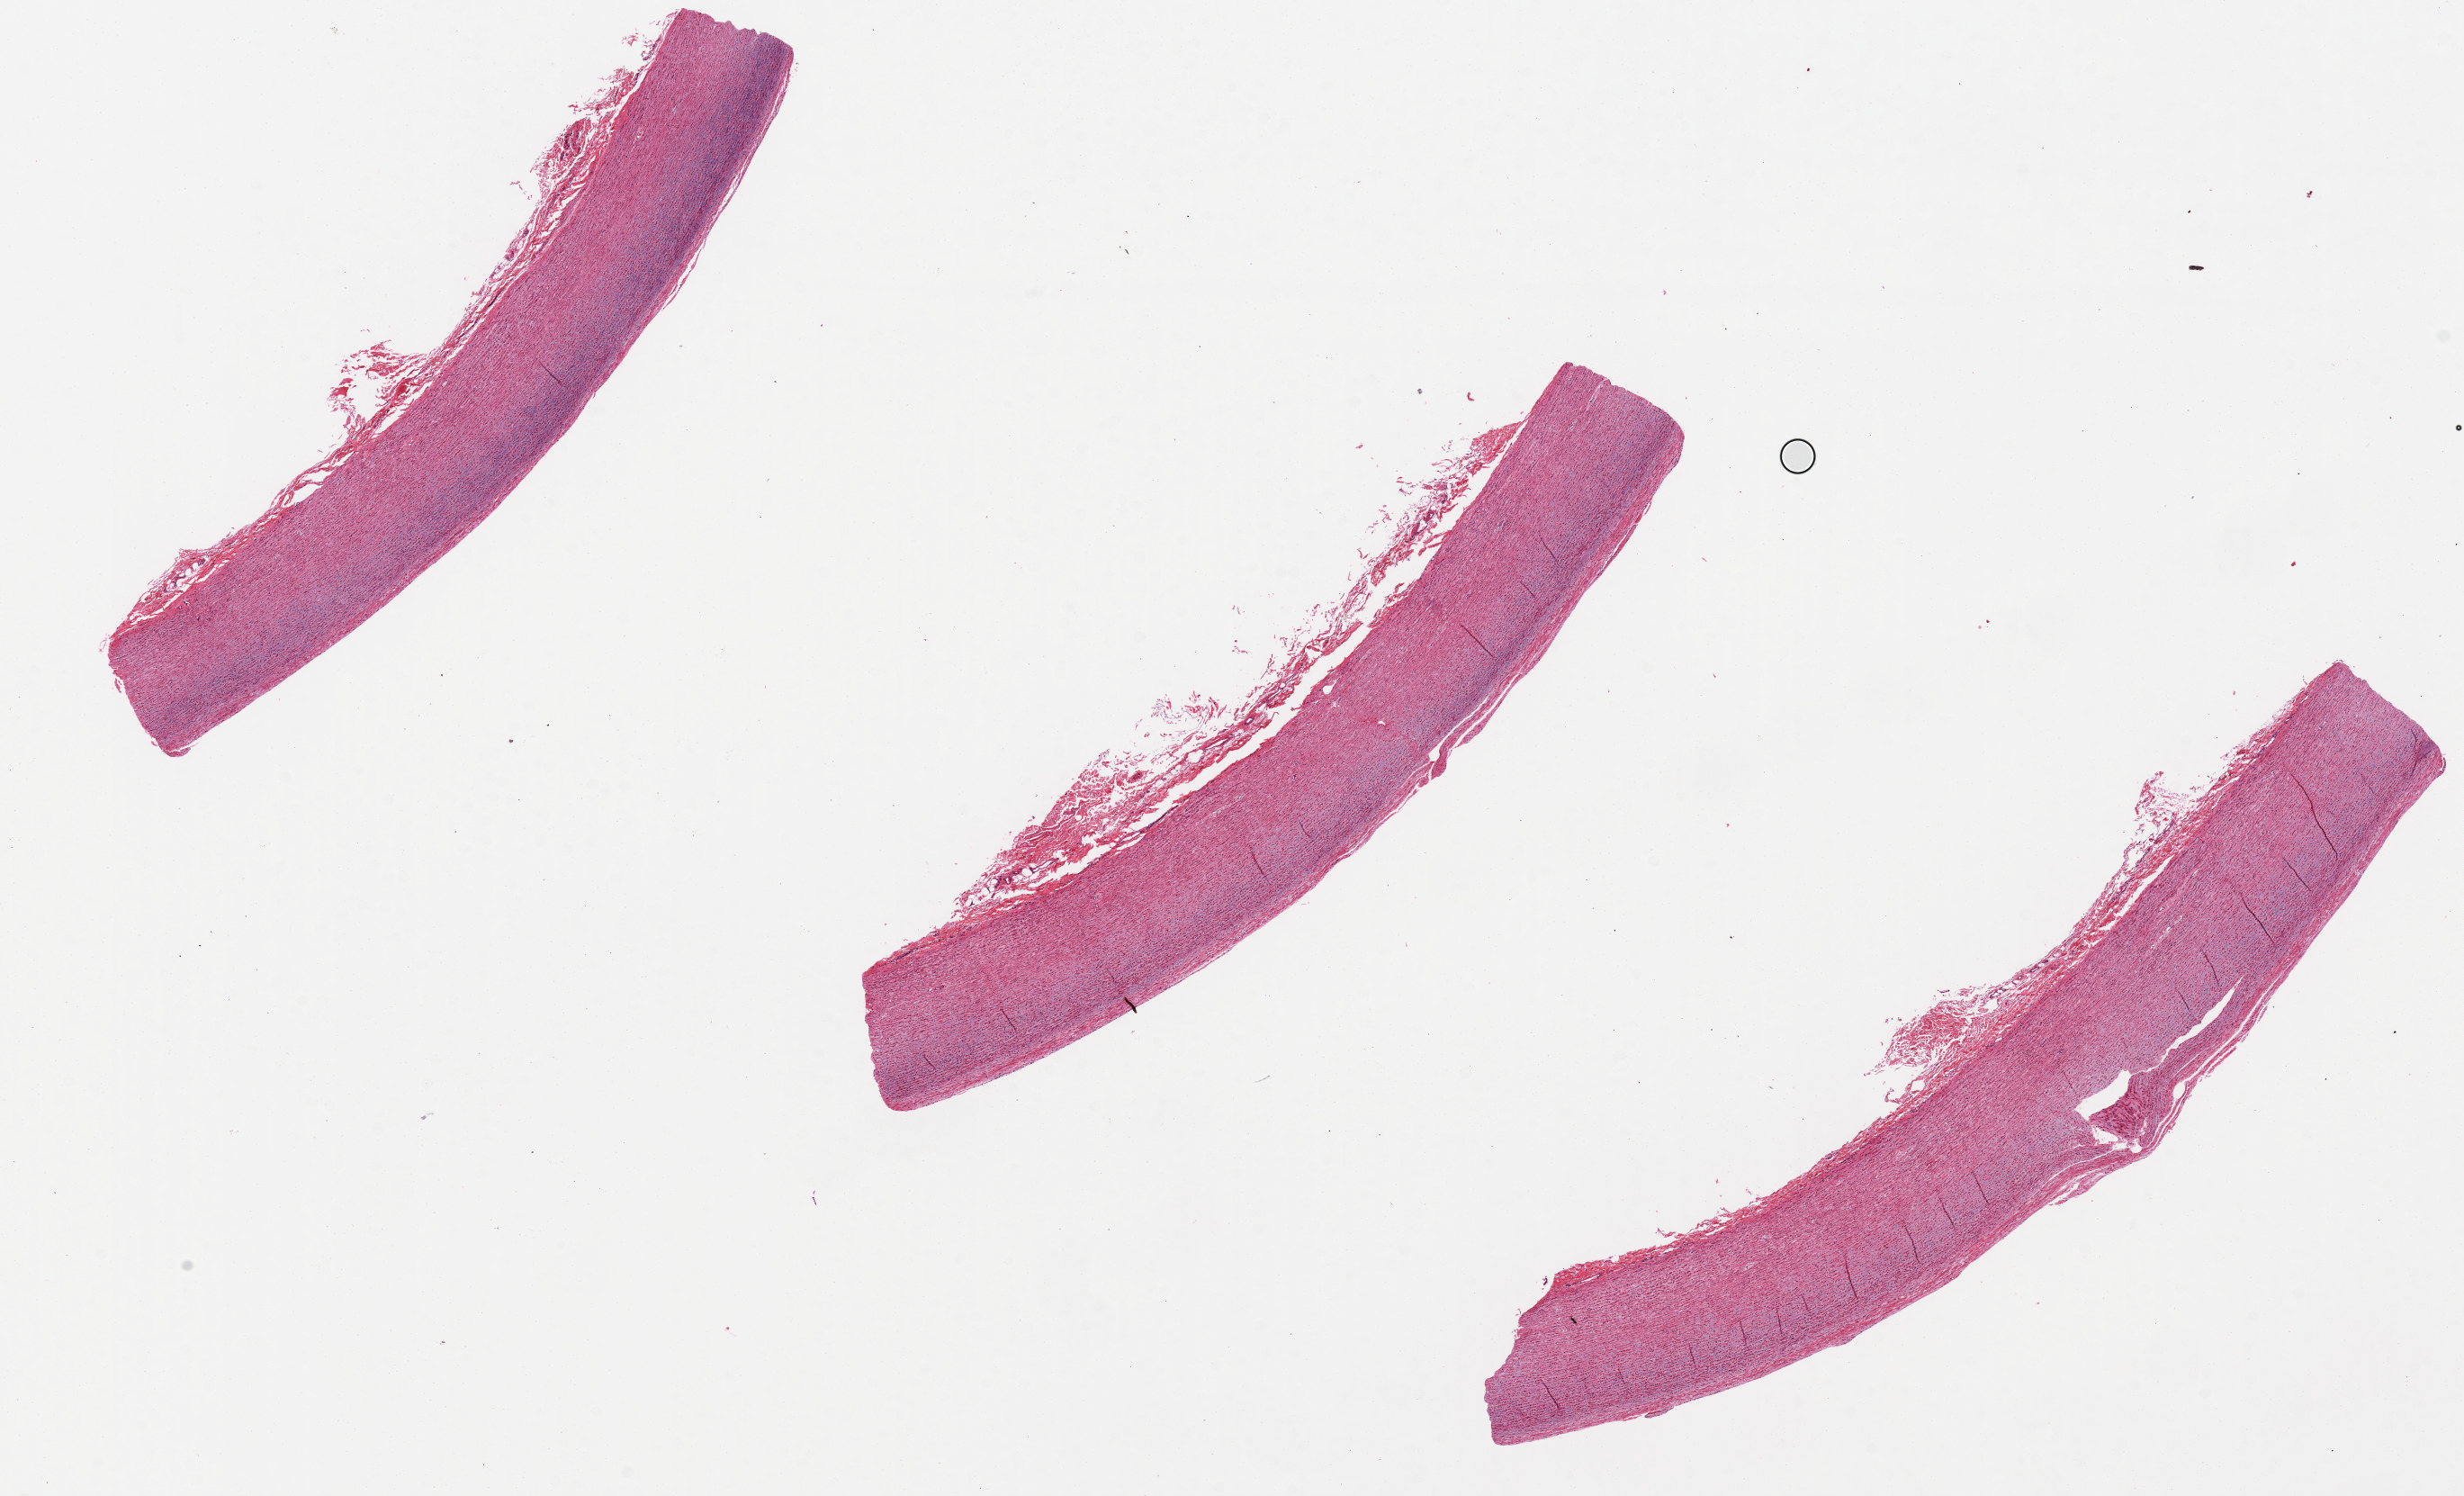
Hematoxylin and eosin (H&E) whole-slide image, shown as a low-resolution overview of the whole scanned area (about 21.7 x 13.1 mm), PAXgene-fixed, paraffin-embedded tissue, sampled site (target tissue): aorta, donor tissue sample. Donor: female.
Pathologist's review note for this sample: Endothelium sloughed. 10 x 1.5mm.